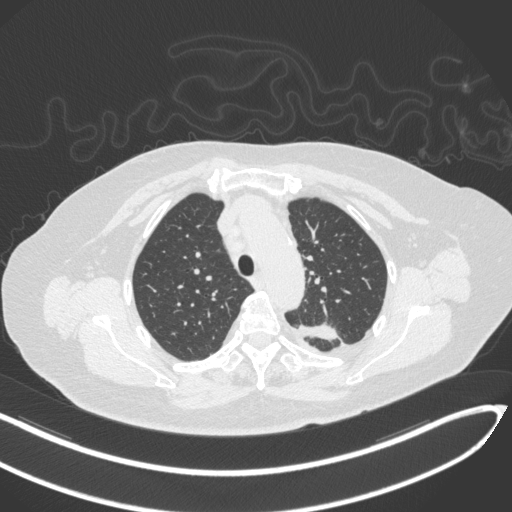
Chest CT, one axial slice; slice 241 of 270 in the series (ordered by position); 120 kVp; lung window (W 1500 / L -600 HU); 1 mm slice thickness; 512 × 512 image matrix, field of view 400 × 400 mm. Female patient, age 76 years. From the clinical record (not read from this slice): clinical TNM (as recorded): T1c N0 M0.
Outlined on this slice (rectangle marked by the reading radiologist):
- lung tumour (recorded histology: adenocarcinoma): bounding box [x1, y1, x2, y2] px = [303, 316, 343, 346]